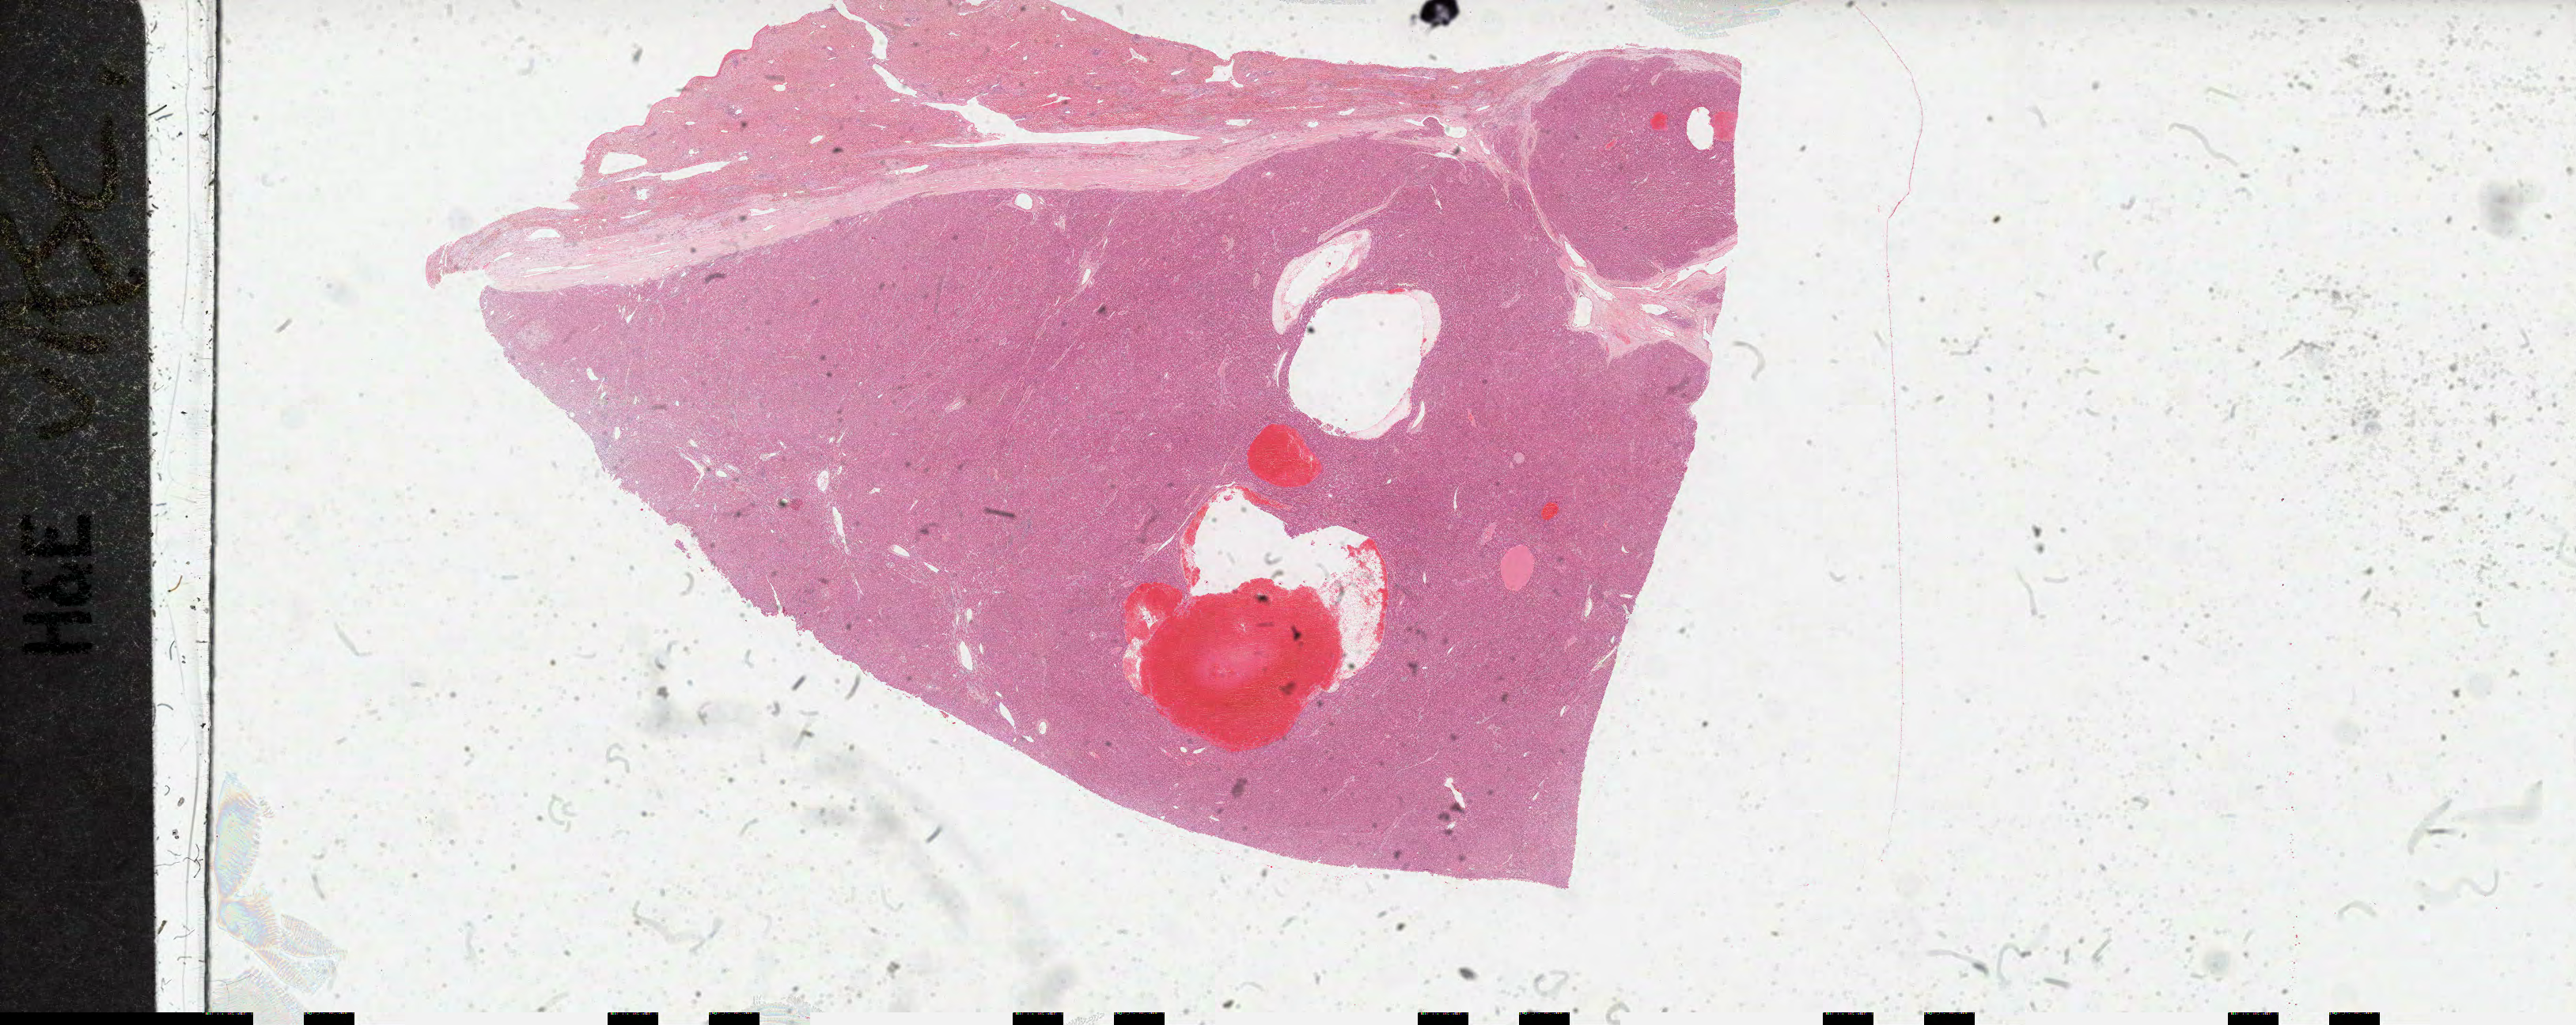
Digitized Hematoxylin and eosin (H&E) stained tissue section (whole slide) — a low-resolution overview of the entire scanned area, about 52.7 x 21.0 mm; formalin-fixed paraffin-embedded (FFPE) diagnostic section; primary tumour sample from the liver. Male patient; age at initial diagnosis 64 years. Histologic grade: G2 (moderately differentiated).
AJCC pathologic stage: II. Pathologic diagnosis: Hepatocellular carcinoma, NOS.